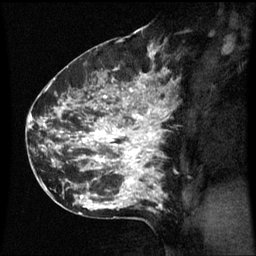
Breast MRI (dynamic contrast-enhanced), one sagittal slice; slice 37 of 60 in the series (ordered by position); dynamic contrast-enhanced series, image 2 of 3 at this slice position (ordered by acquisition); 1.5 T; TE 4.2 ms, TR 8.9 ms; 256 × 256 image matrix. Patient: female, 42 years. Case-level facts recorded for this patient, not image findings: setting: breast cancer imaged before/during neoadjuvant chemotherapy; receptor status: HER2-positive.
Outlined on this slice (semi-automatic segmentation, software-assisted and operator-edited):
- analysis volume of interest (the breast-tissue region the enhancement analysis was run in; not a lesion): bounding box <66,82,171,193> (left, top, right, bottom; pixels)
- tumour enhancement mask (voxels above the 70 % enhancement threshold inside the analysis volume of interest): <76,82,169,193>